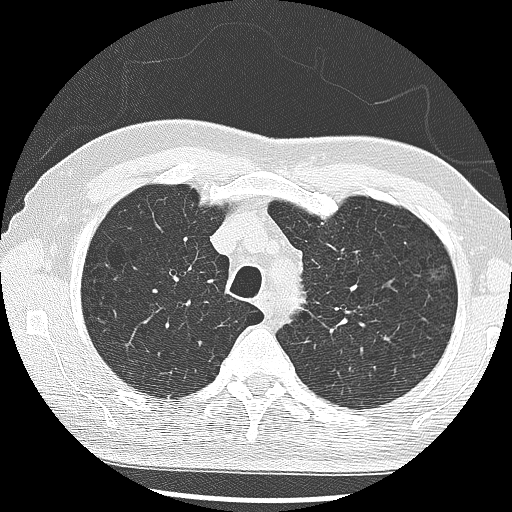
Low-dose screening chest CT, one axial slice. Slice 221 of 285 in the series (ordered by position). Reconstruction kernel LUNG. Lung window (W 1500 / L -600 HU). 2.5 mm slice thickness. 512 × 512 image matrix.
Annotated regions visible in this slice (manually delineated by an expert):
- lesion 1 (tumor, upper lobe of left lung): box from (x=429, y=264) to (x=449, y=283) px